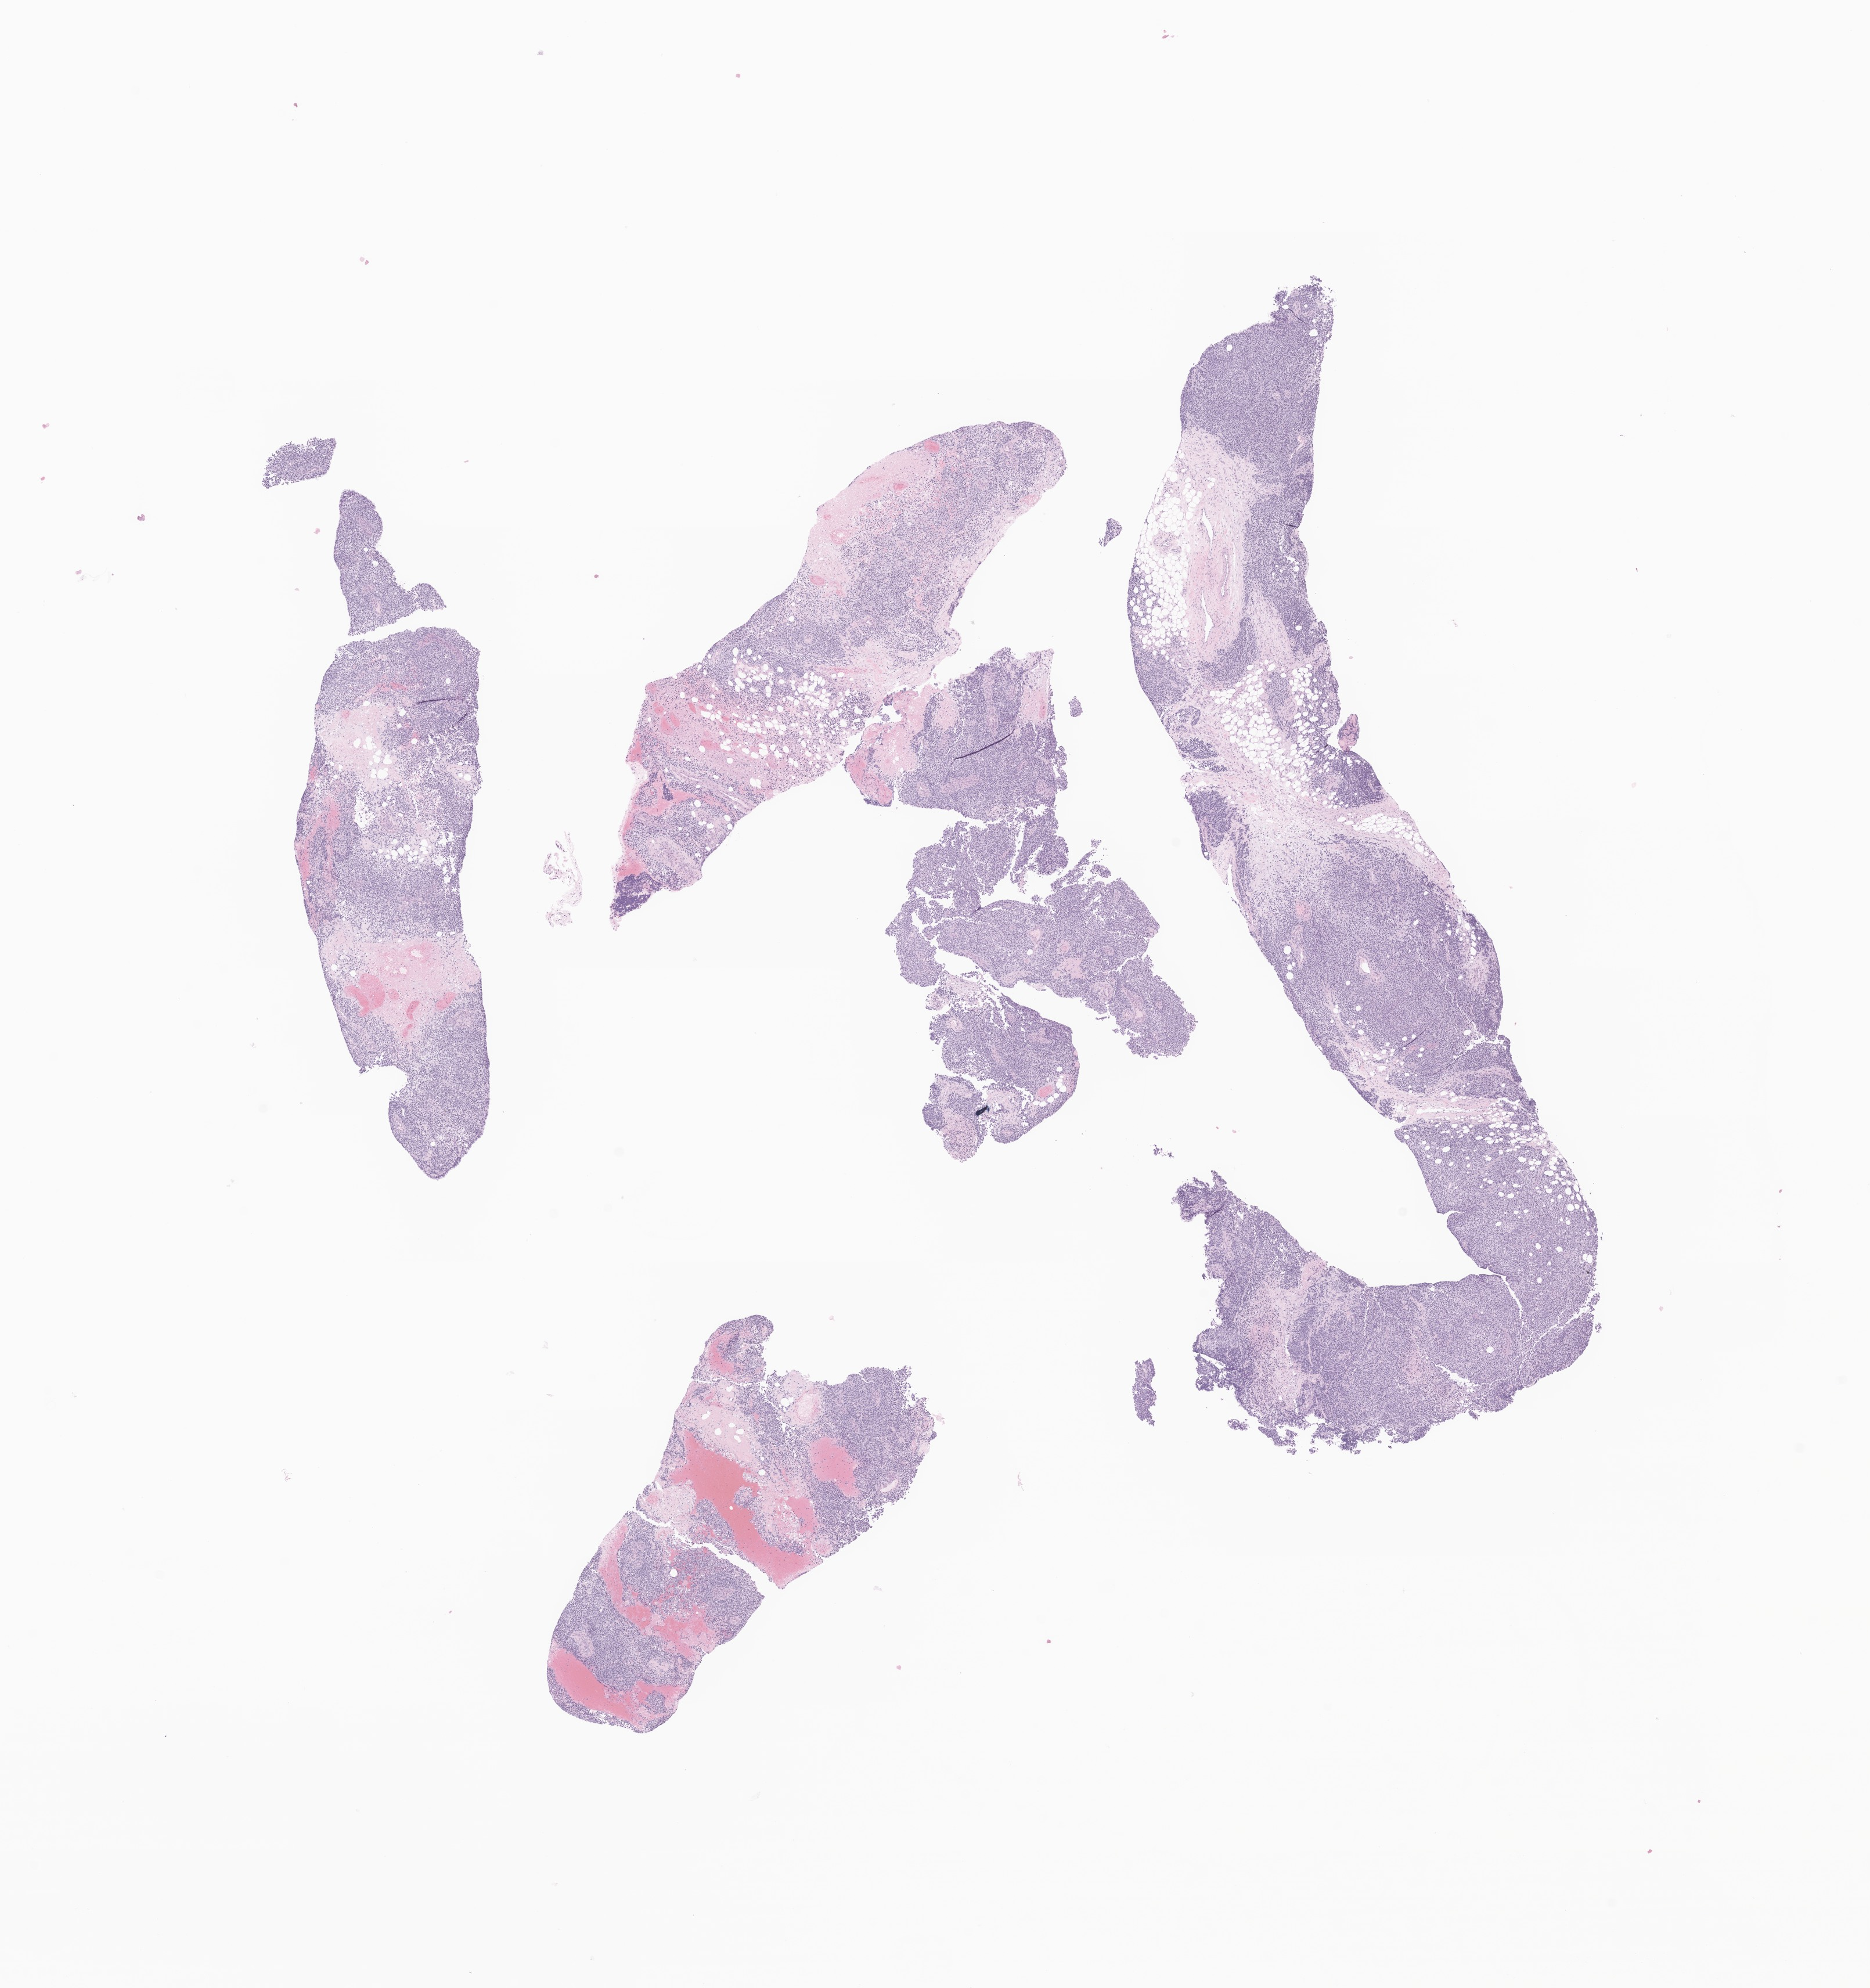
Digitized H&E-stained section of tumor tissue from the mediastinum — shown as a low-resolution overview of the whole scanned area (about 13.6 x 14.4 mm); formalin-fixed paraffin-embedded section. Female patient, age 181 months (15 years 1 month).
Diagnosis (ICD-O-3 morphology term): Neoplasm, malignant.